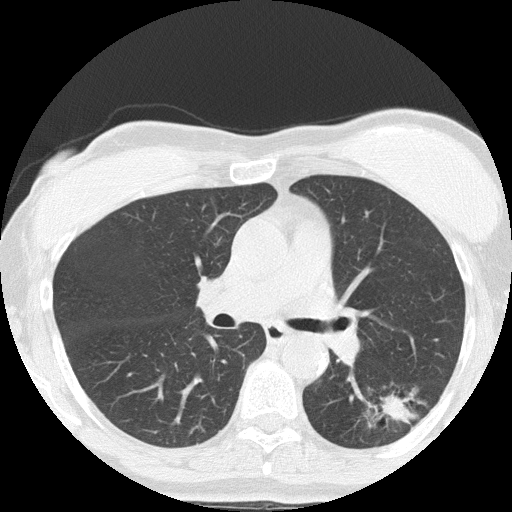
Low-dose screening chest CT, one axial slice; slice 89 of 152 in the series (ordered by position); reconstruction kernel FC51; 120 kVp; lung window (W 1500 / L -600 HU); 2 mm slice thickness; 512 × 512 image matrix, field of view 308 × 308 mm.
Outlined on this slice (expert manual segmentation):
- lesion 1 (tumor, lower lobe of left lung): bounding box [x1, y1, x2, y2] px = [383, 394, 407, 421]